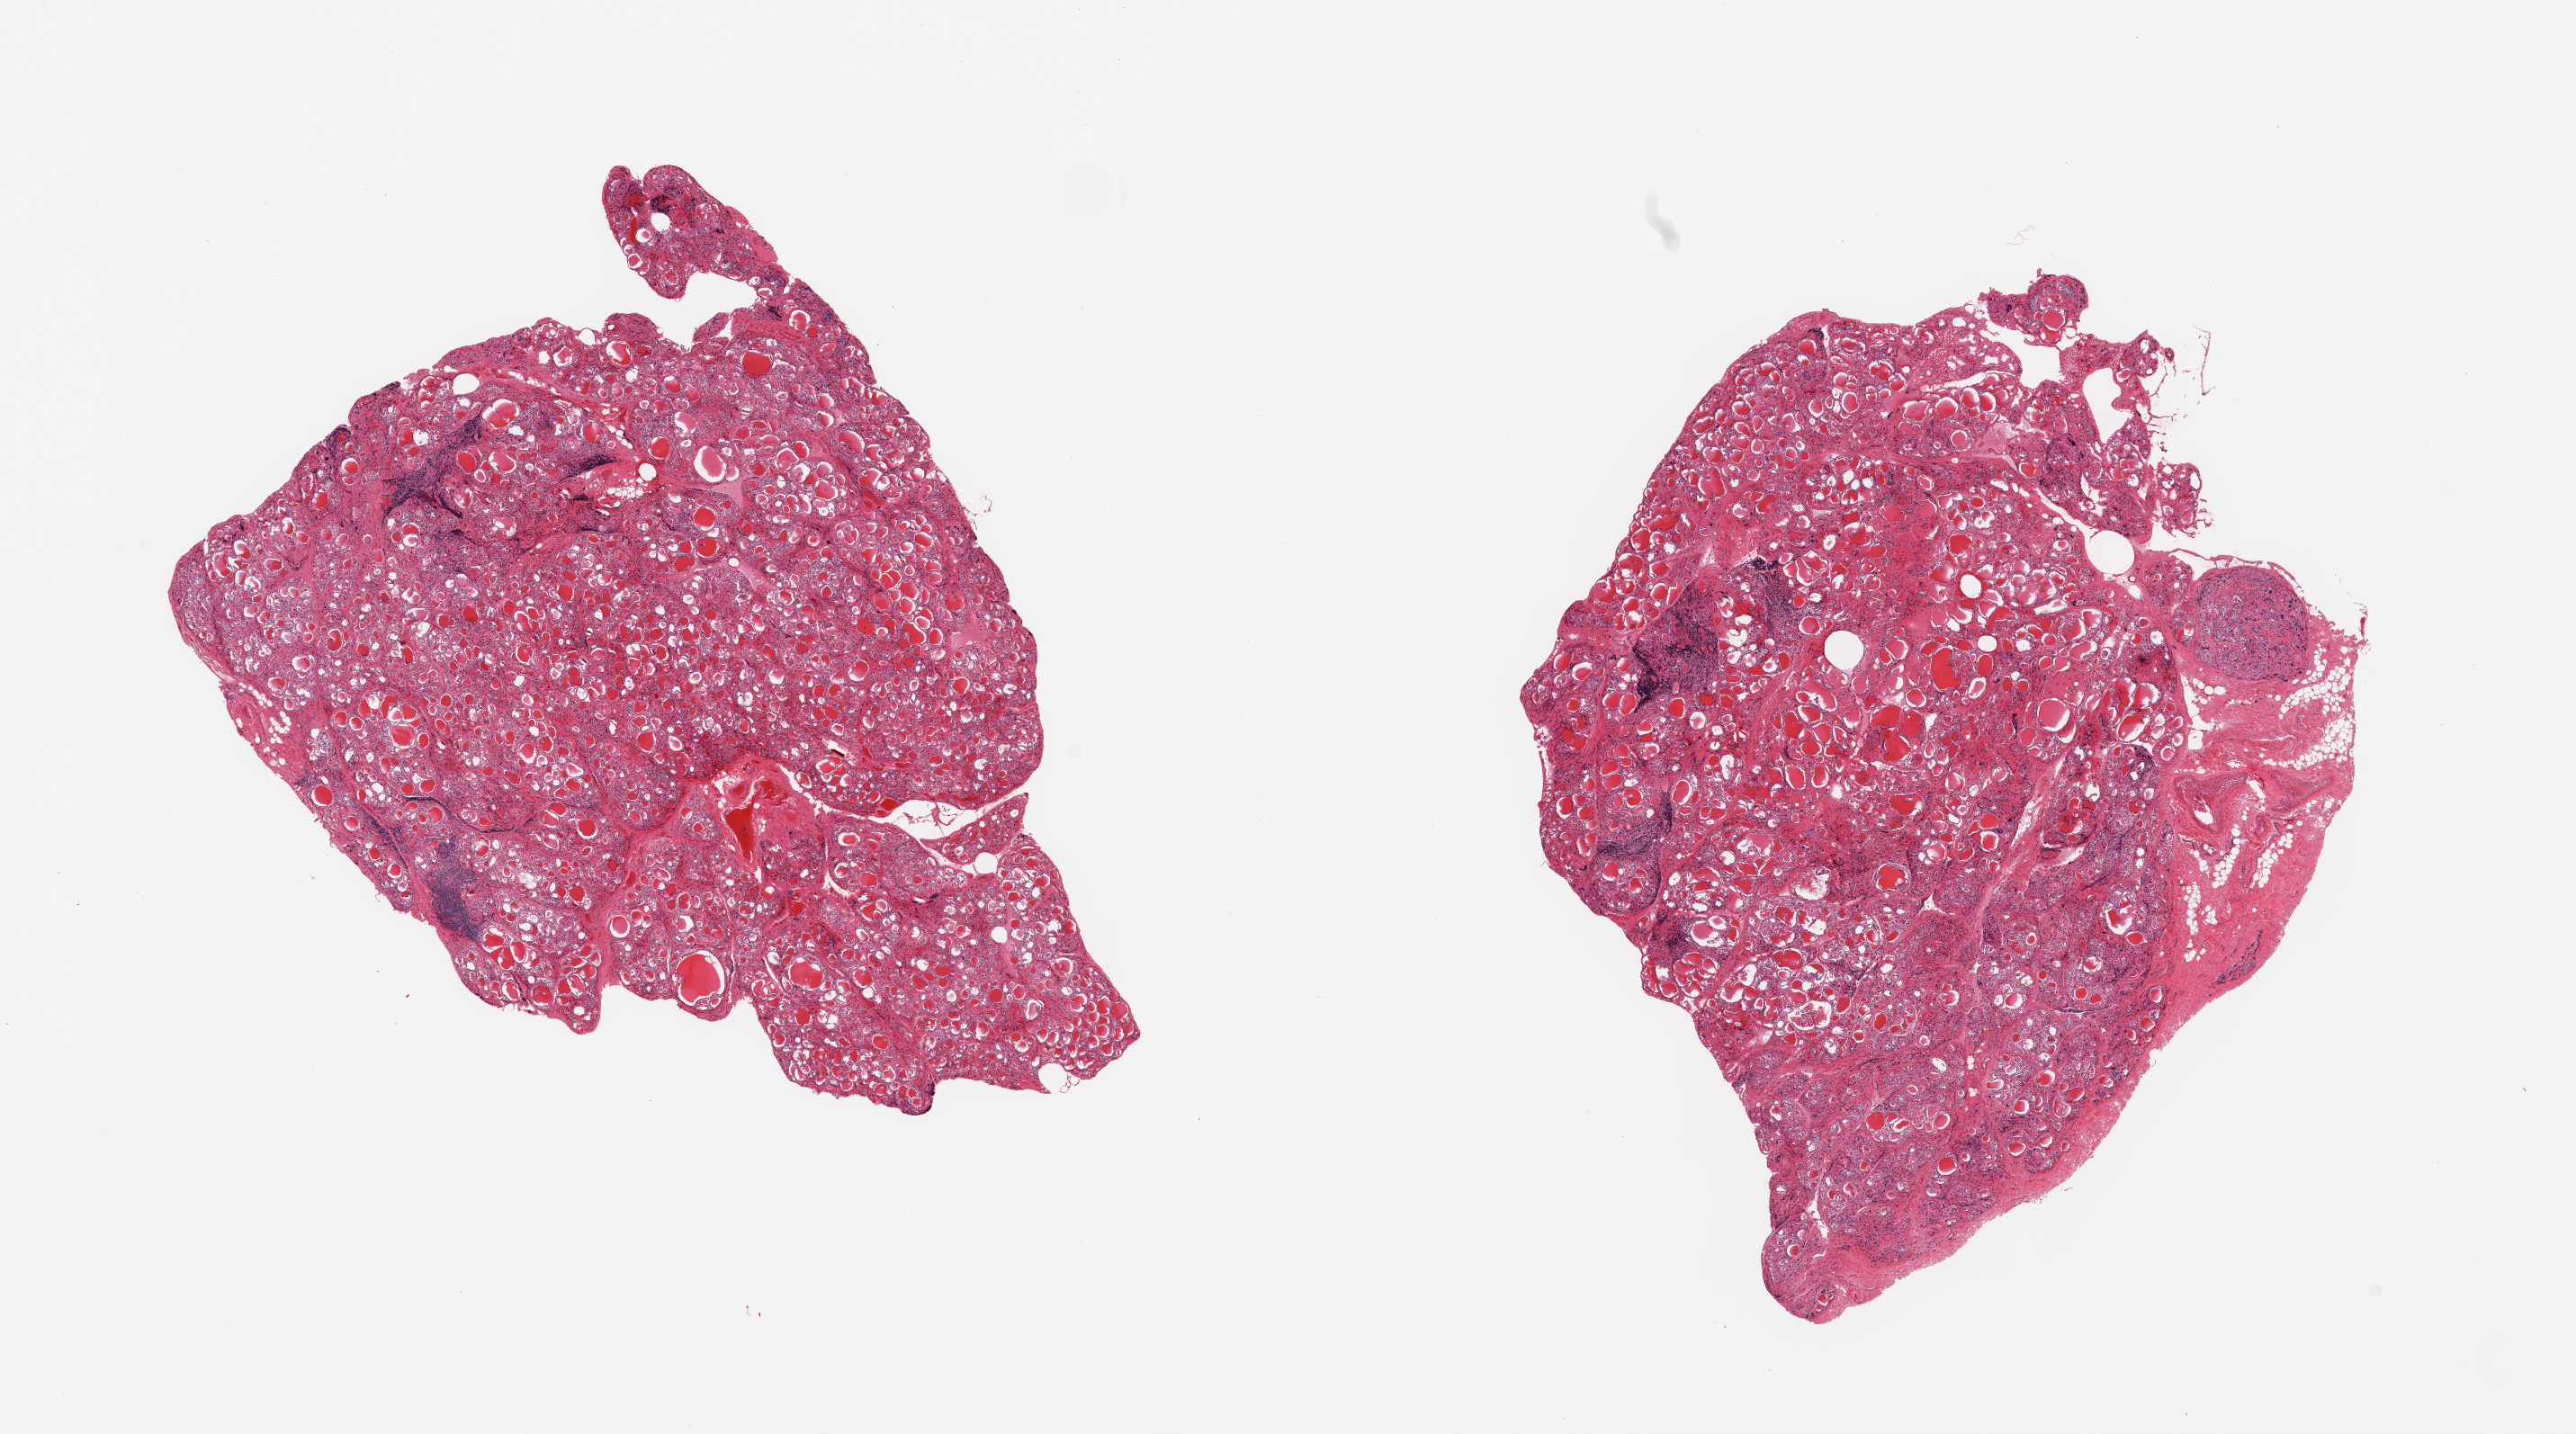
Whole-slide image, haematoxylin and eosin stain — a low-resolution overview of the entire scanned area, about 22.6 x 12.6 mm (acquisition: 20x scan), PAXgene-fixed, paraffin-embedded tissue, sampled site (target tissue): thyroid, donor tissue sample. Donor: female.
- review note (as recorded): 2 pieces, lymphoid aggregates and regressive changes suggest Hashimoto/autoimmune thyroiditis; Possible poorly preserved parathyroid